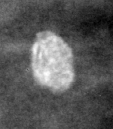
Region of interest cut from a scanned film mammogram (one marked finding); right breast; CC view; BI-RADS breast density category 2 (scale 1–4).
Finding: calcifications, morphology coarse / round and regular / lucent center; BI-RADS assessment category 2; benign without callback (not worked up further).